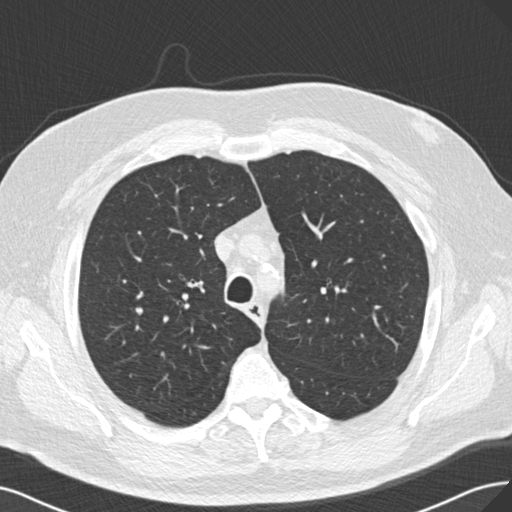
Low-dose screening chest CT, axial slice, first (baseline) screen, lung window (W 1500 / L -600 HU), 2 mm slice thickness, standard (soft-tissue) reconstruction kernel (B30f). Male participant, aged 67 years at enrolment.
• Expert reader's lesion annotation, bounding box <130,302,146,319> (left, top, right, bottom; pixels).
• No non-calcified nodule or mass ≥4 mm was recorded by the screening reader at this exam.
• Official screen result: negative screen, minor abnormalities not suspicious for lung cancer.
• Later outcome: lung cancer diagnosed 561 days after this screen — small cell carcinoma, NOS, right middle lobe, stage IA (AJCC 6th edition), 20 mm at pathology.